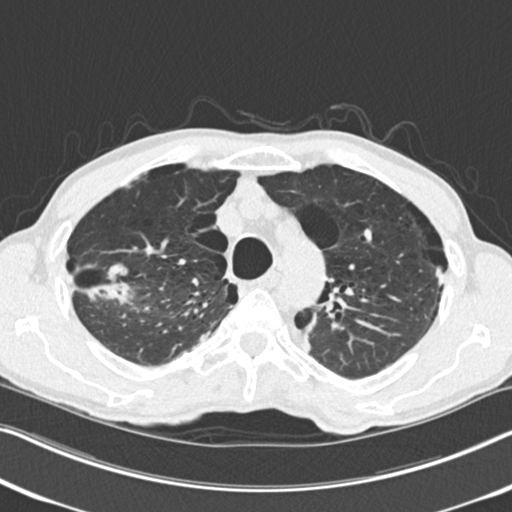
Low-dose screening chest CT, axial slice, second screening round (one year after baseline), lung window (W 1500 / L -600 HU), 2 mm slice thickness, 120 kVp, slice 60 of 251 in the series. Male participant, aged 71 years at enrolment.
Expert-annotated lung lesion, box from (x=70, y=249) to (x=143, y=319) px. The screening reader recorded 4 non-calcified nodules or masses ≥4 mm on this exam (right upper lobe, right upper lobe, right upper lobe, left upper lobe); which of them this box marks is not recorded. Lung cancer was diagnosed 83 days after this screen: adenocarcinoma, NOS, right upper lobe, well differentiated (G1), stage IA (AJCC 6th edition), 30 mm at pathology.